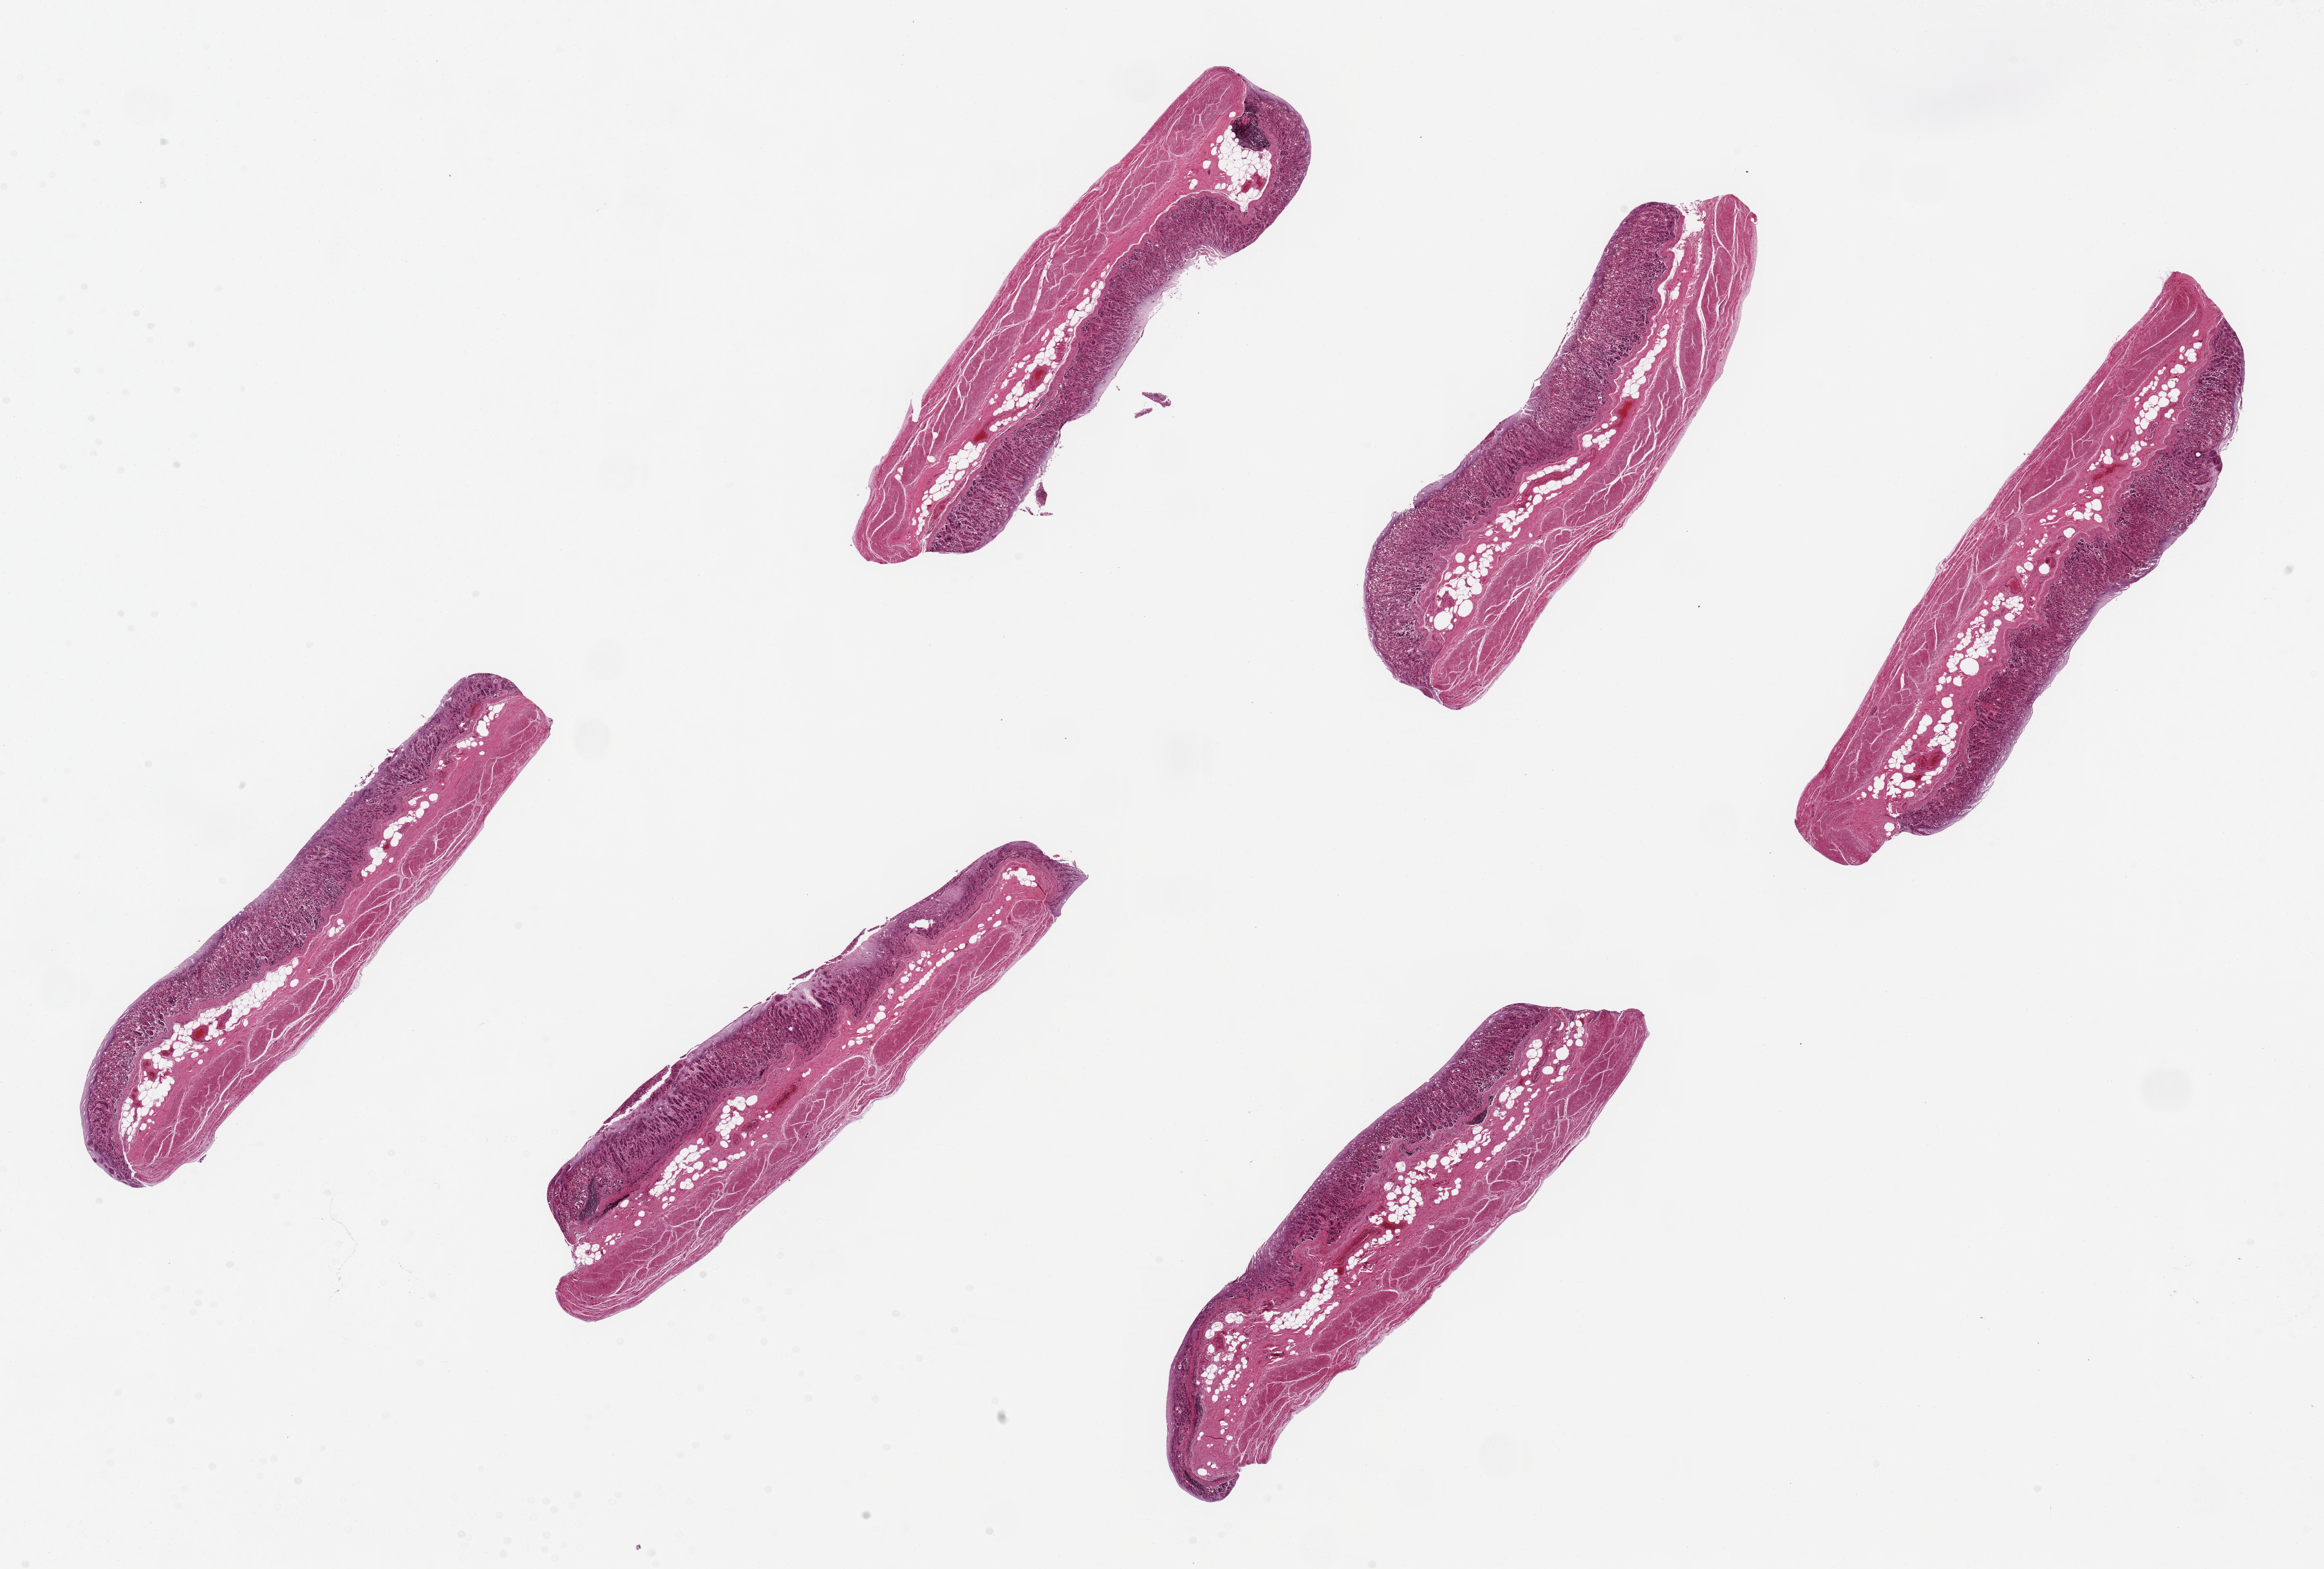
Digitized H&E-stained section, whole scanned area (about 28.5 x 19.3 mm) shown as a low-resolution overview. PAXgene-fixed, paraffin-embedded tissue. Target tissue: stomach. Tissue donor sample. Female donor.
* review note (as recorded): 6 pieces, ~8x1.5mm. Mucosa moderately autolyzed; superficial layer completely necrotic, ? relationship to drug overdose